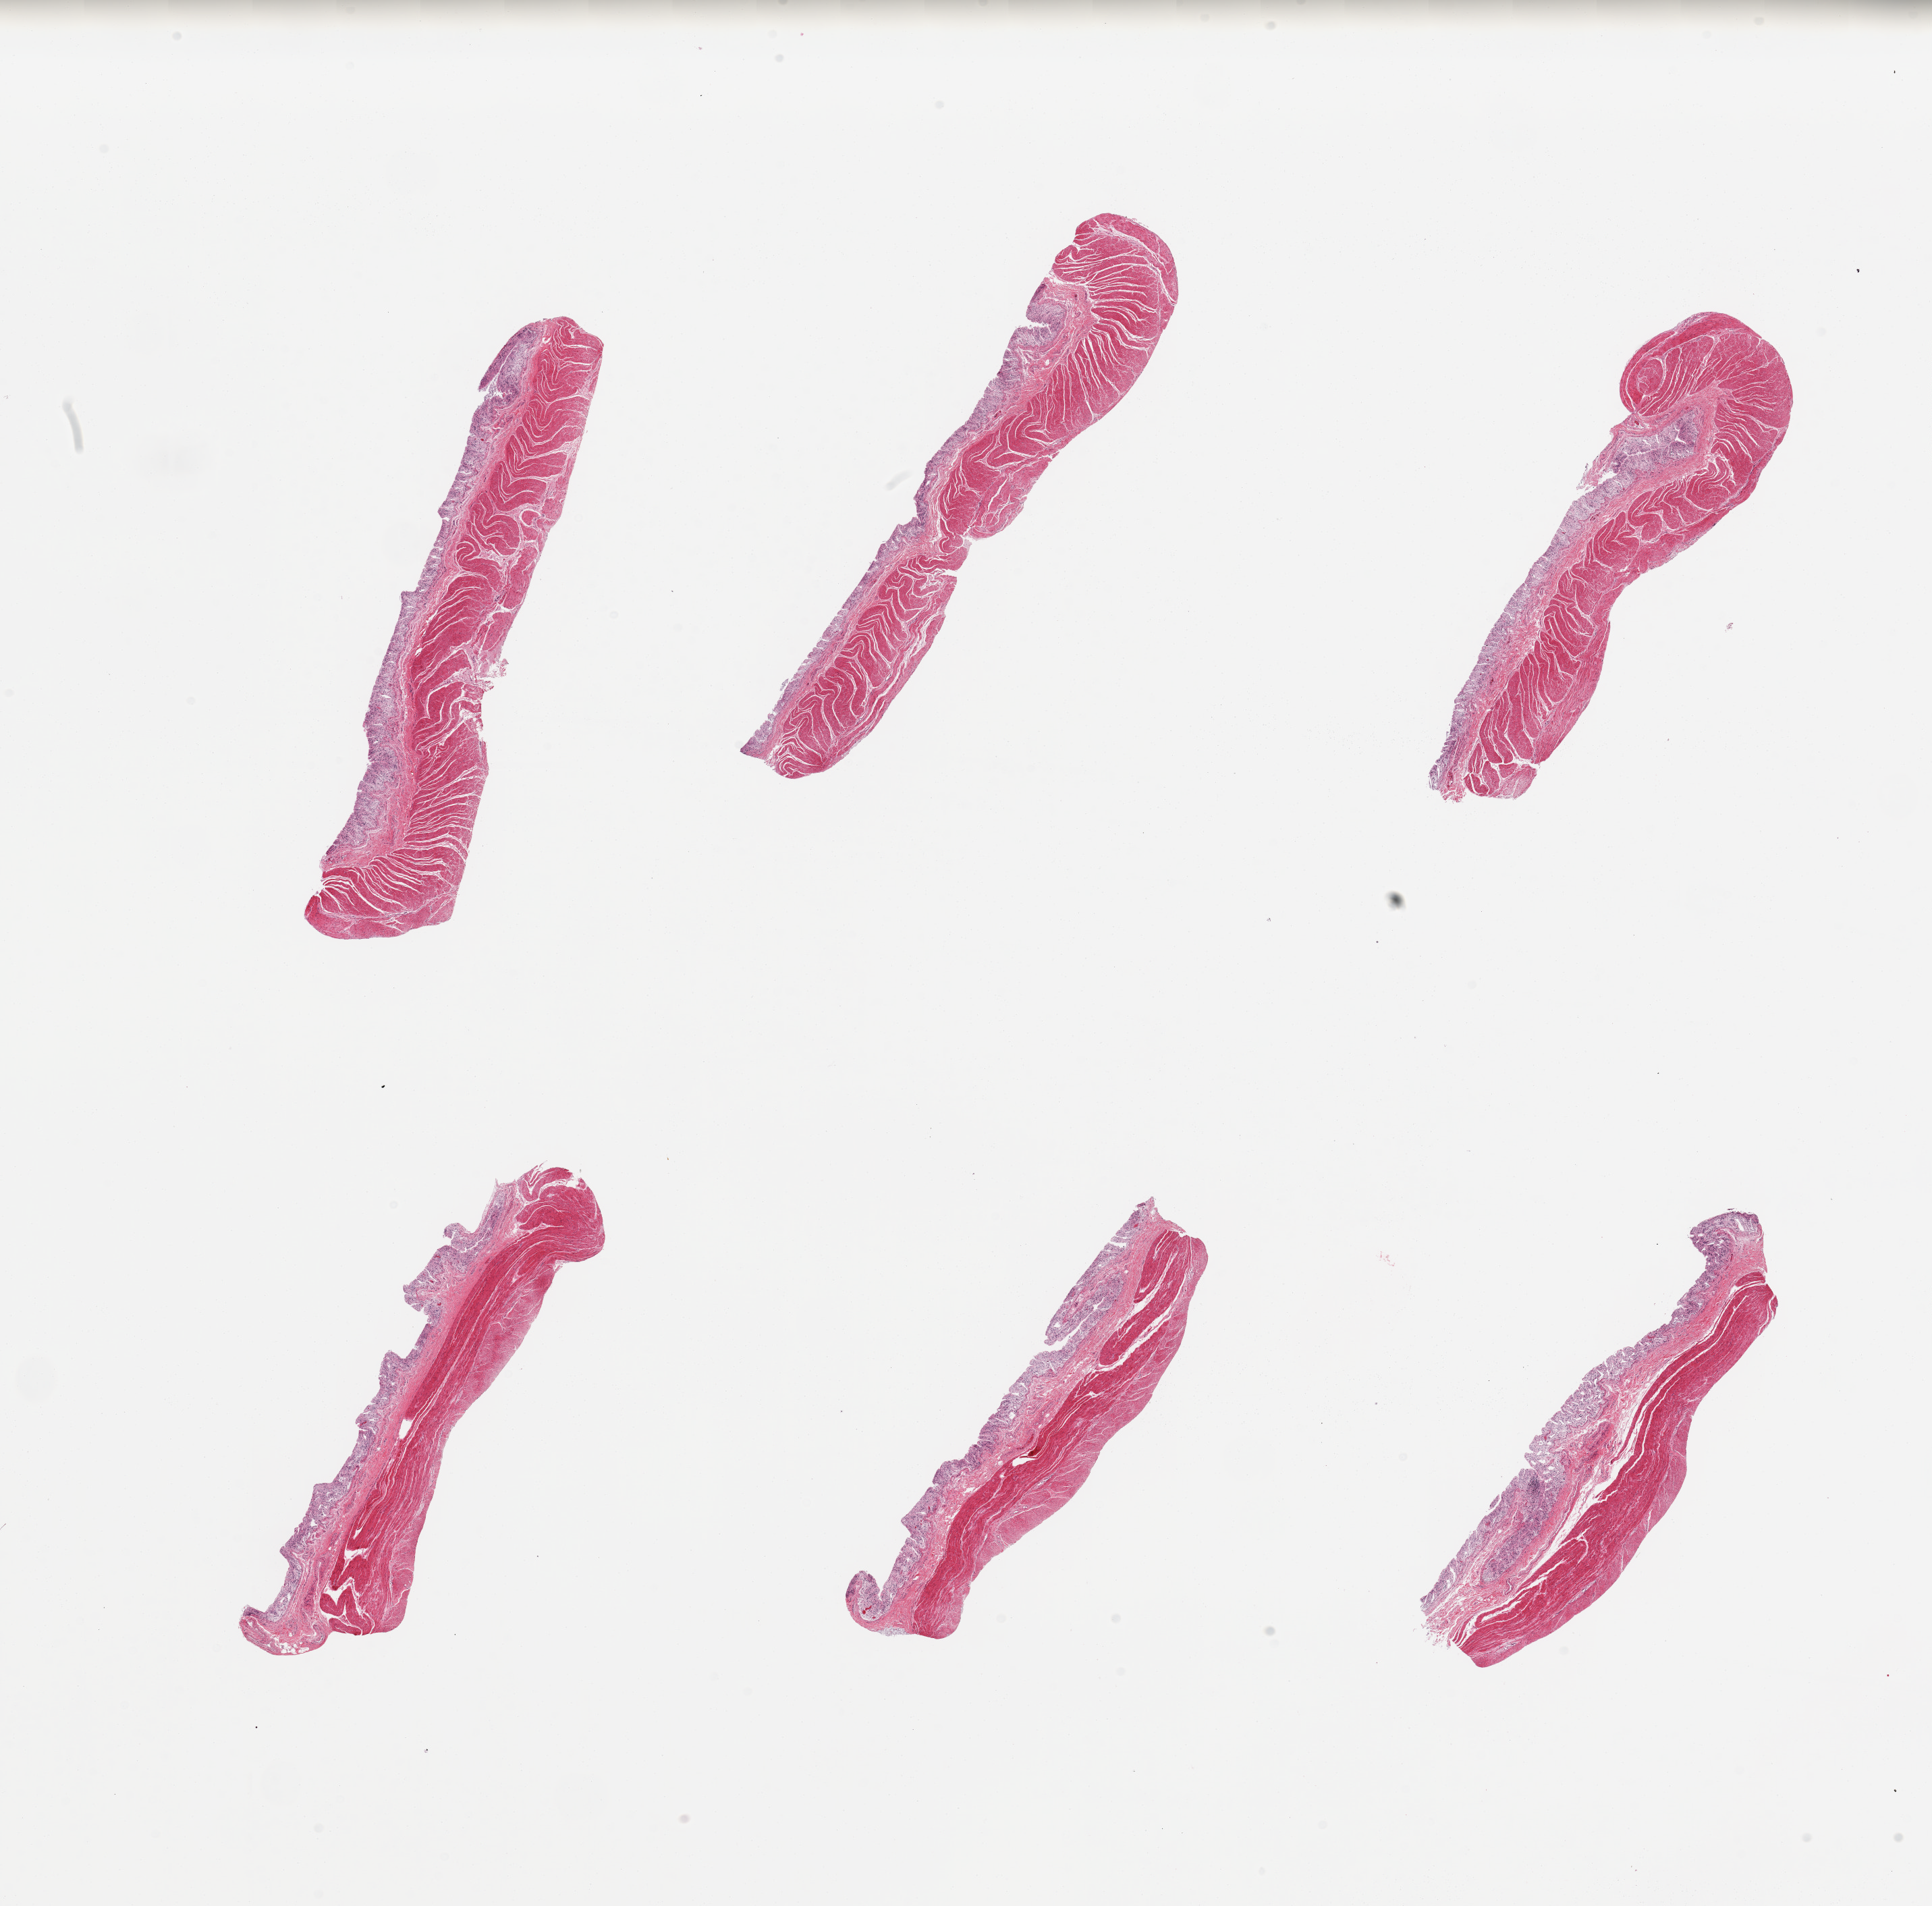
Whole-slide image, haematoxylin and eosin stain — shown as a low-resolution overview of the whole scanned area (about 22.6 x 22.3 mm); PAXgene-fixed paraffin-embedded (PFPE) section; target tissue: sigmoid colon; donor tissue sample. Male donor.
• review note (as recorded): 6 pieces; muscularis (target) and severely autolyzed mucosa (not target)